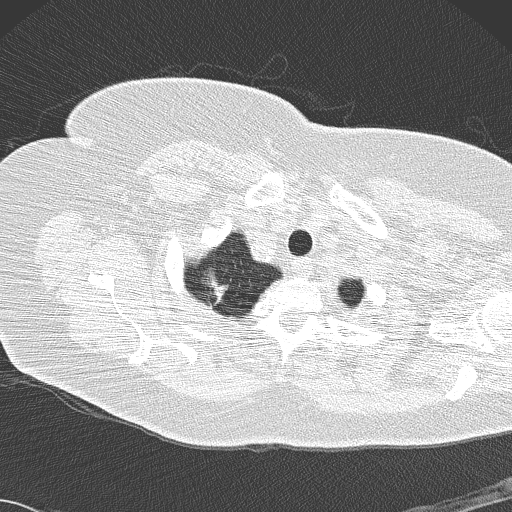
Axial slice from a low-dose chest CT screening exam; second annual screen; lung window (W 1500 / L -600 HU). Female participant, aged 72 years at enrolment. Former smoker at enrolment.
Lesion marked by an expert reader, box from (x=183, y=247) to (x=257, y=326) px. The screening reader recorded 4 non-calcified nodules or masses ≥4 mm on this exam; which of them this box marks is not recorded. Official screen result: positive, other. Lung cancer was diagnosed 52 days after this screen: bronchiolo-alveolar adenocarcinoma, NOS, right upper lobe, stage IIIB (AJCC 6th edition), 45 mm at pathology.